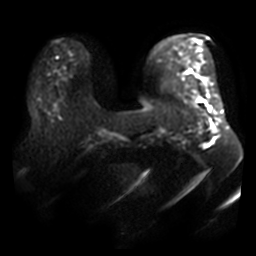
Breast MRI, one axial slice; position 11 of 40 along the scan axis; diffusion-weighted series; image 2 of 4 stored at this slice position (different b-values; order by instance number); 3 T; 256 × 256 image matrix, field of view 400 × 400 mm. Female patient.
Outlined on this slice (manually delineated by an expert):
- tumour on diffusion-weighted imaging: bounding box [x1, y1, x2, y2] px = [213, 126, 219, 133]